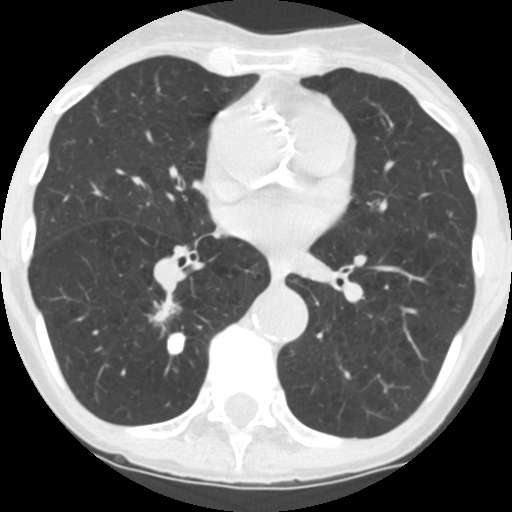
Low-dose screening chest CT, one axial slice; position 59 of 124 along the scan axis; reconstruction kernel STANDARD; 120 kVp; lung window (W 1500 / L -600 HU); 2.5 mm slice thickness; 512 × 512 image matrix, field of view 260 × 260 mm.
Structures marked on this image (outlined manually by an expert reader):
- lesion 1 (tumor, lower lobe of right lung): bounding box <154,305,175,322> (left, top, right, bottom; pixels)